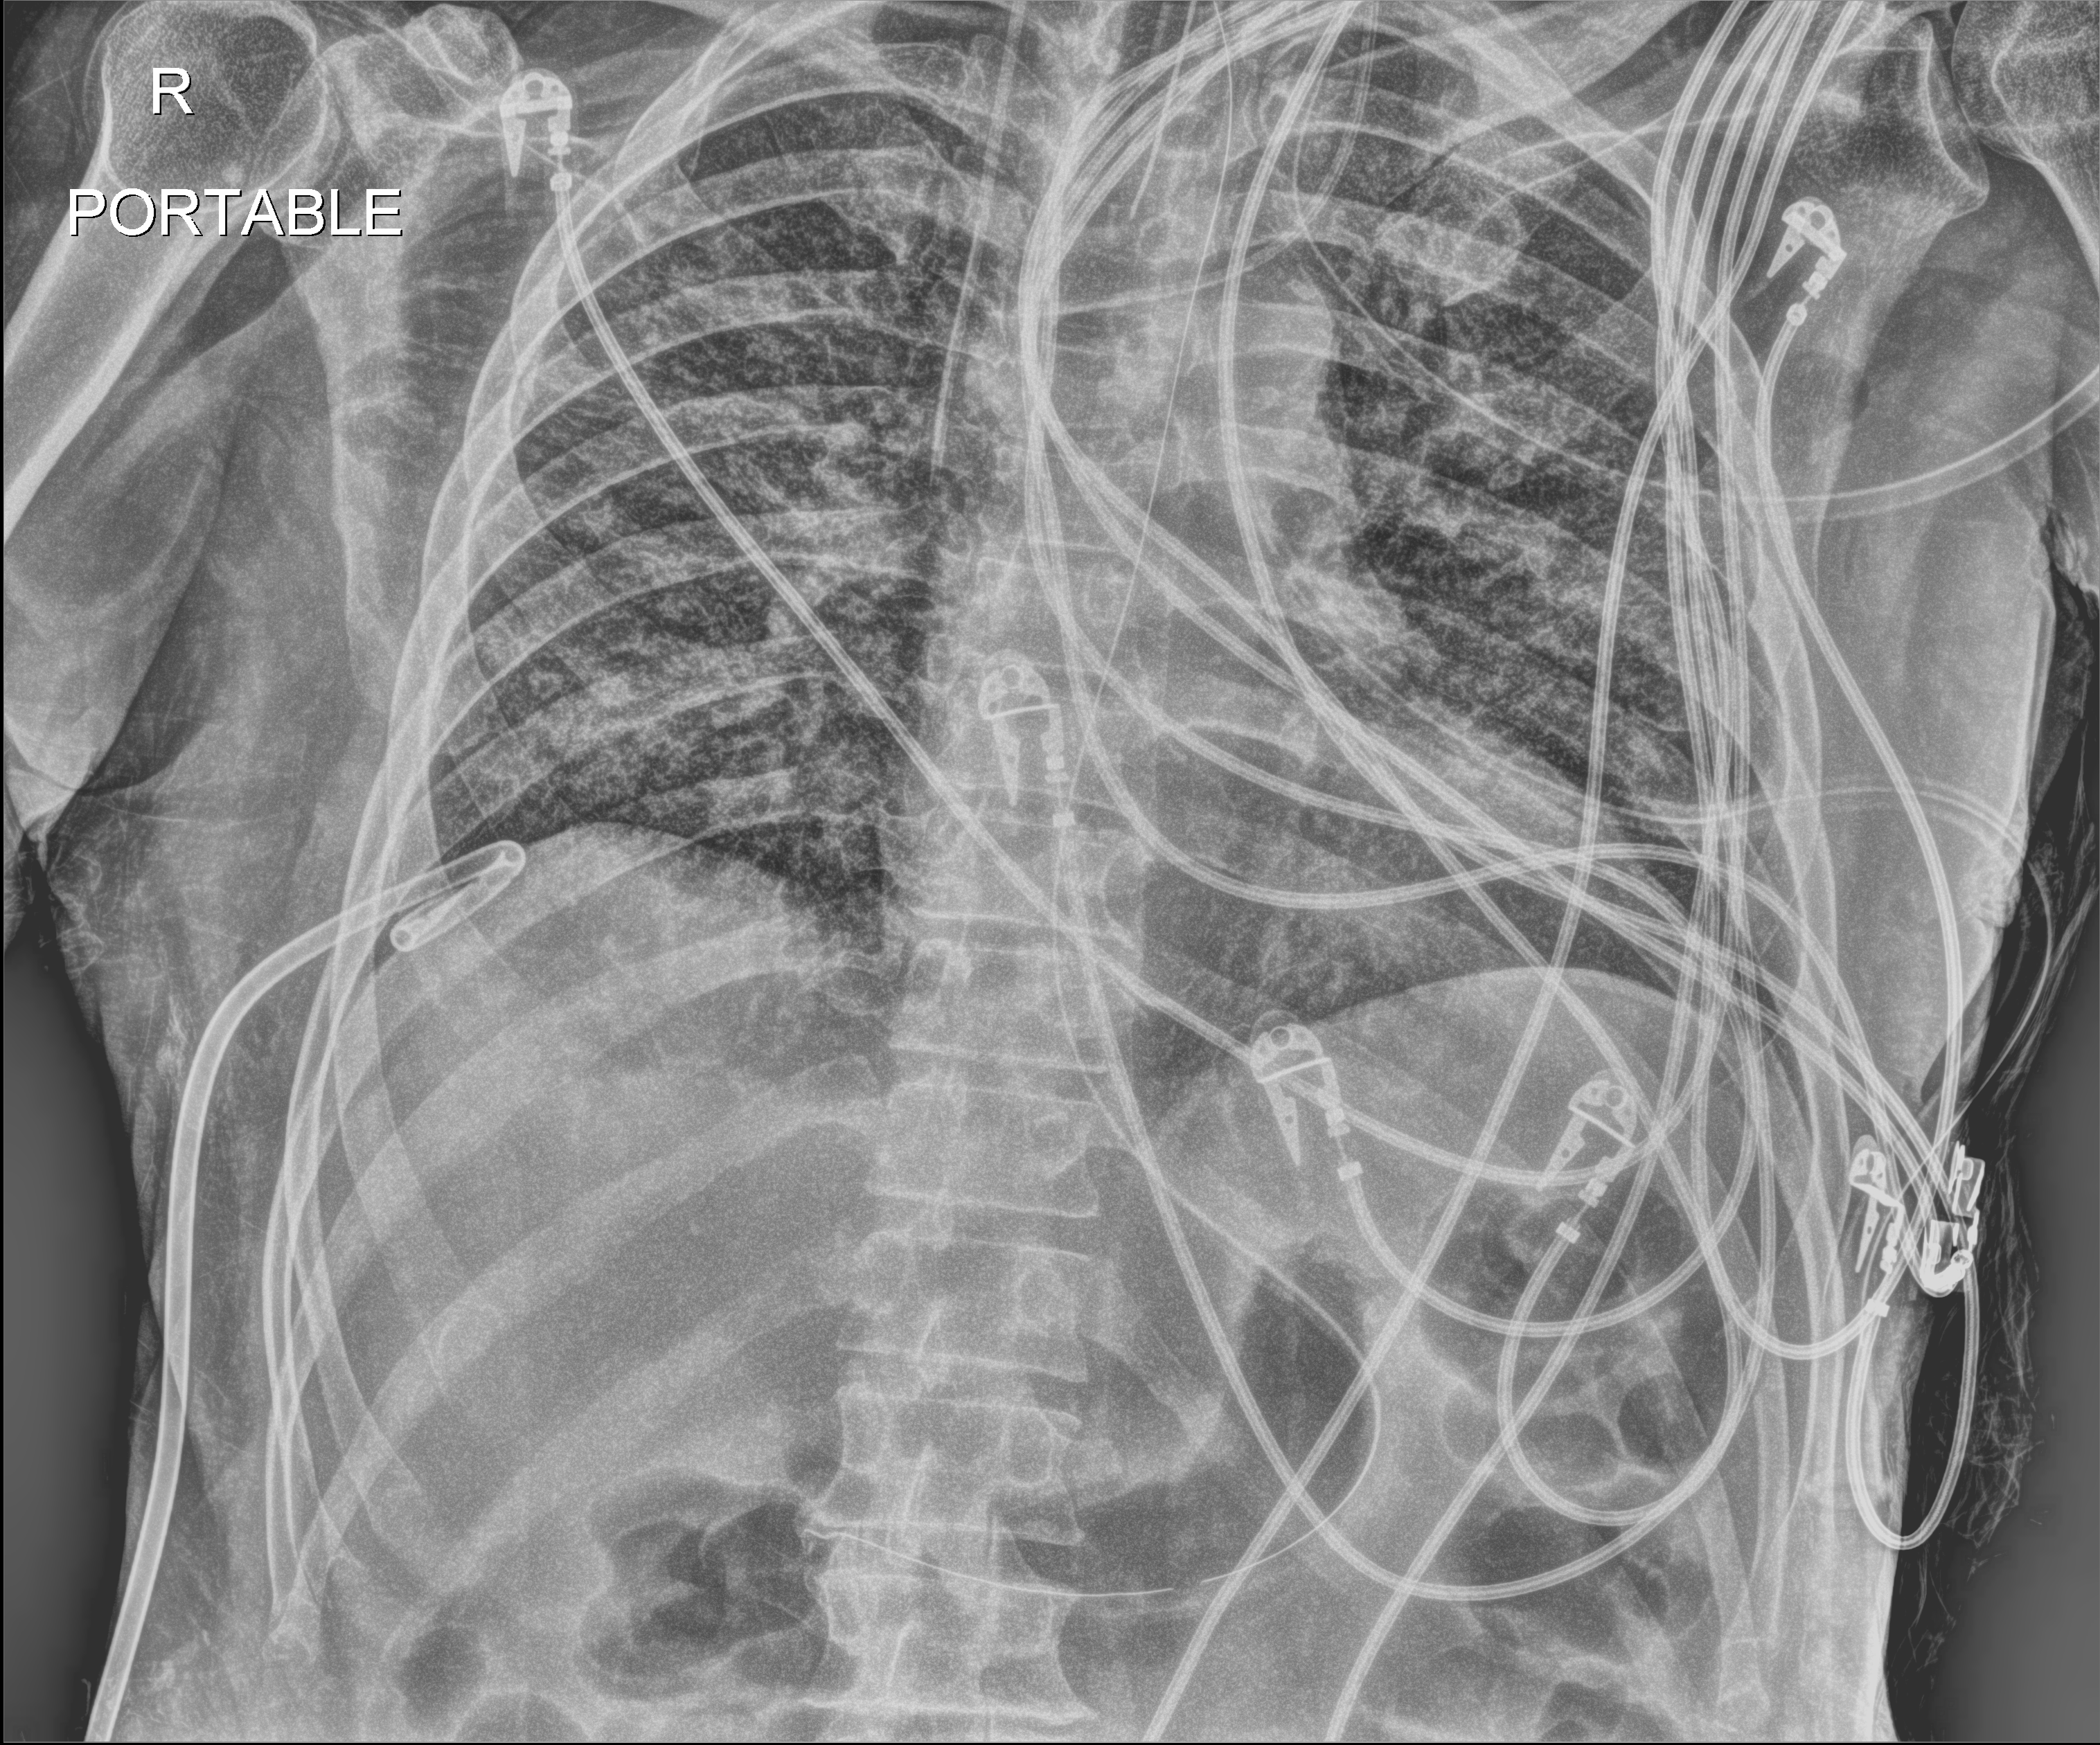
Chest X-ray (portable), anteroposterior (AP) projection. Patient hospitalised with COVID-19; male, aged 18–59 years.
From the hospital-stay record, not from the radiograph (when in the stay this image was taken is not recorded): smoking status (admission record): never; COPD (admission record): no; length of hospital stay: 77 days.